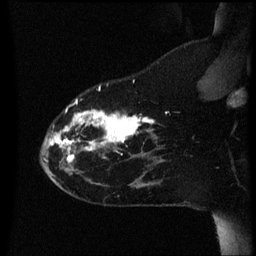
Breast MRI (dynamic contrast-enhanced), one sagittal slice; position 14 of 60 along the scan axis; dynamic contrast-enhanced series, image 2 of 3 at this slice position (ordered by acquisition); 1.5 T; TE 4.2 ms, TR 8.4 ms; 2.2 mm slice thickness; 256 × 256 image matrix, field of view 200 × 200 mm. Female patient, age 35 years. Case-level facts recorded for this patient, not image findings: setting: breast cancer imaged before/during neoadjuvant chemotherapy; receptor status: HER2-positive.
Structures marked on this image (semi-automatic segmentation, software-assisted and operator-edited):
- analysis volume of interest (the breast-tissue region the enhancement analysis was run in; not a lesion): bounding box (x1, y1, x2, y2) in pixels: (42, 78, 168, 173)
- tumour enhancement mask (voxels above the 70 % enhancement threshold inside the analysis volume of interest): (46, 86, 156, 163)